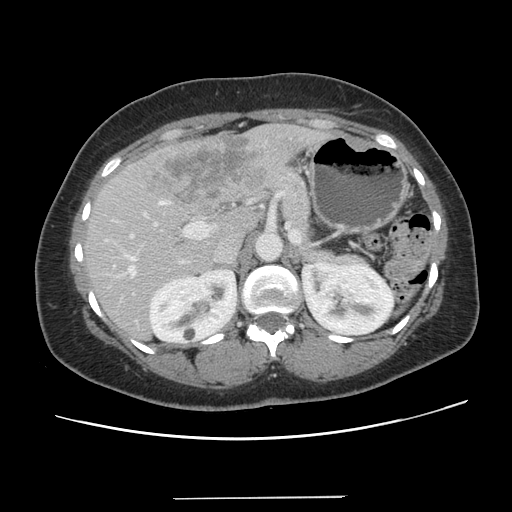
Contrast-enhanced abdominal CT, one axial slice; intravenous contrast given; soft-tissue window (W 400 / L 40 HU); 512 × 512 image matrix, field of view 366 × 366 mm. Female patient, age 53 years. Case-level facts recorded for this patient, not image findings: diagnosis: colorectal cancer liver metastases, imaged before liver resection; multiple liver metastases: no; largest metastasis: 14.5 cm.
Annotated regions visible in this slice (manually delineated by an expert):
- hepatic veins: bounding box (x1, y1, x2, y2) in pixels: (125, 253, 135, 276)
- liver: (86, 124, 323, 340)
- planned liver remnant (the part of the liver to remain after resection): (87, 205, 258, 340)
- portal vein (with intrahepatic branches): (130, 200, 212, 238)
- liver metastasis: (149, 135, 266, 207)